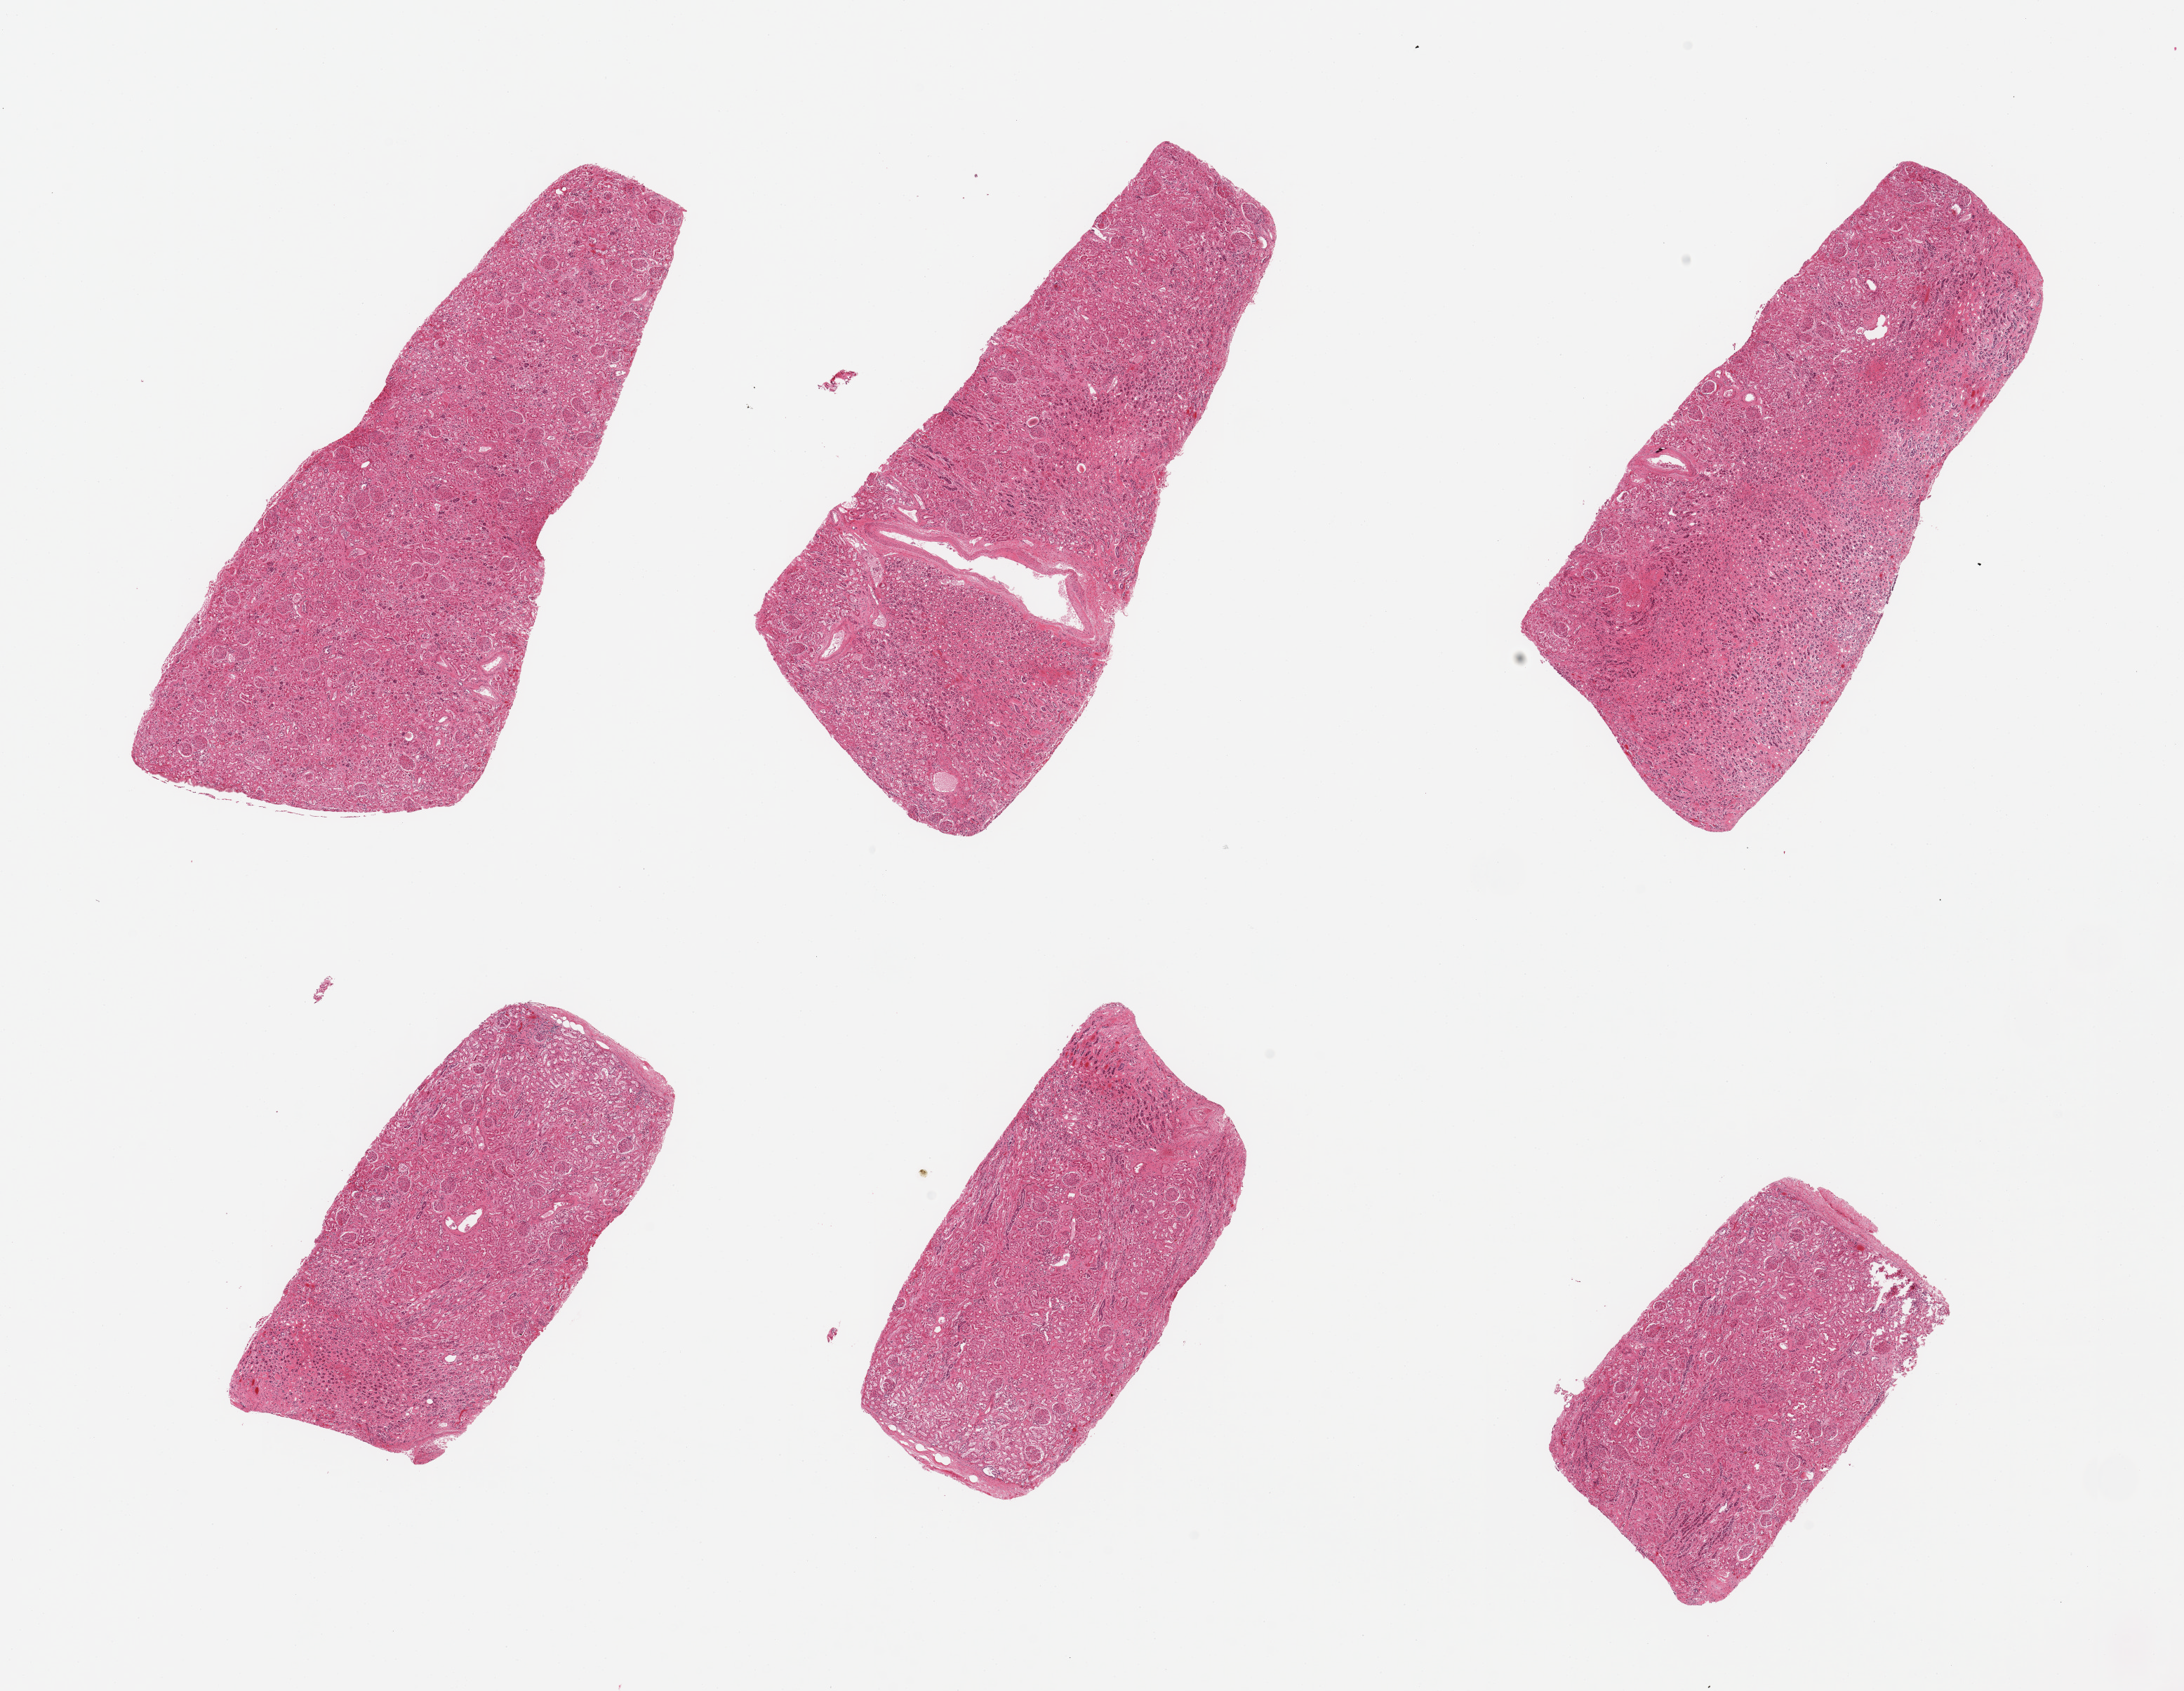
Digitized haematoxylin and eosin-stained section, a low-resolution overview of the entire scanned area, about 24.6 x 19.1 mm. PAXgene-fixed paraffin-embedded (PFPE) section. Sampled site (target tissue): renal cortex. Tissue donor sample. Donor: male.
Review note (as recorded): 6 pieces; no active or chronic lesions; up to 40% admixture with medulla.